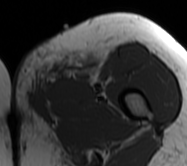
MRI of an extremity soft-tissue mass, one axial slice. Slice 15 of 62 in the series (ordered by position). MR volume resampled by the dataset authors to the PET/CT grid (not the native acquisition matrix). 3.27 mm slice thickness. 187 × 166 image matrix, field of view 183 × 162 mm. Female patient. Case-level facts recorded for this patient, not image findings: histological type: leiomyosarcoma; grade: high; site of the primary tumour: groin.
Structures marked on this image (expert contour drawn on MRI and transferred to this co-registered scan by the dataset authors):
- gross tumour volume including surrounding oedema: box from (x=11, y=42) to (x=97, y=120) px
- gross tumour volume (mass): (x=66, y=60)–(x=94, y=81)